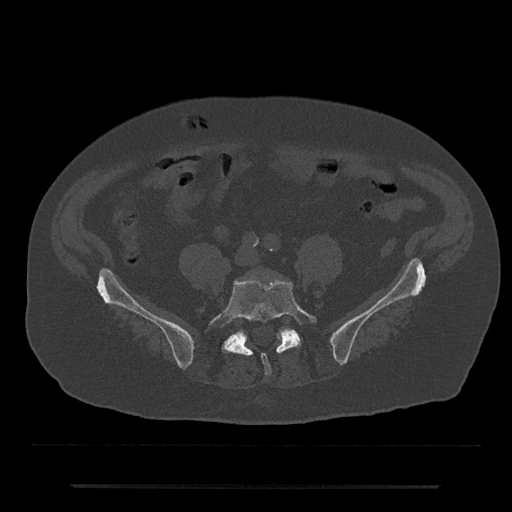
CT including the spine, one axial slice; reconstruction kernel Br40s/3; bone window (W 1800 / L 400 HU); 0.5 mm slice thickness; 512 × 512 image matrix. Male patient, age 80 years. From the clinical record (not read from this slice): primary cancer: prostate.
Outlined on this slice (semi-automatically segmented with operator editing):
- L5 vertebra: box from (x=209, y=277) to (x=317, y=376) px